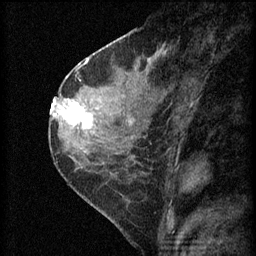
Breast MRI (dynamic contrast-enhanced), one sagittal slice. Slice 28 of 60 in the series (ordered by position). 3 images stored at this slice position (order not interpretable as contrast timing). 1.5 T. TE 4.2 ms, TR 8.2 ms. 256 × 256 image matrix. Female patient, age 45 years.
Structures marked on this image (semi-automatic segmentation, software-assisted and operator-edited):
- analysis volume of interest (the breast-tissue region the enhancement analysis was run in; not a lesion): box from (x=62, y=98) to (x=104, y=139) px
- tumour enhancement mask (voxels above the 70 % enhancement threshold inside the analysis volume of interest): (x=62, y=102)–(x=94, y=129)